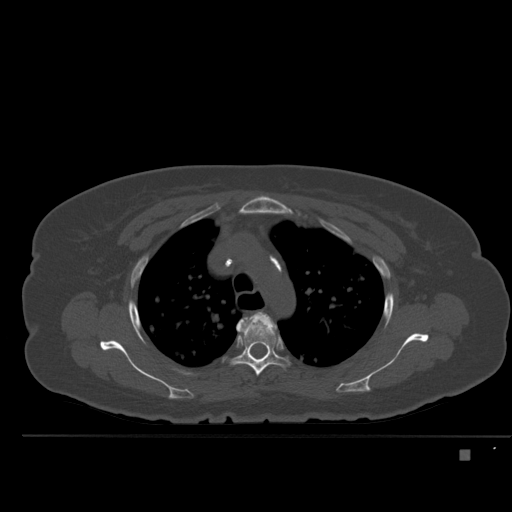
CT including the spine, one axial slice; position 369 of 477 along the scan axis; bone window (W 1800 / L 400 HU); 1.5 mm slice thickness; 512 × 512 image matrix, field of view 422 × 422 mm. Patient: female, 74 years. From the clinical record (not read from this slice): primary cancer: colon.
Outlined on this slice (semi-automatically segmented with operator editing):
- T3 vertebra: bounding box <236,311,278,344> (left, top, right, bottom; pixels)
- T4 vertebra: <232,317,288,377>